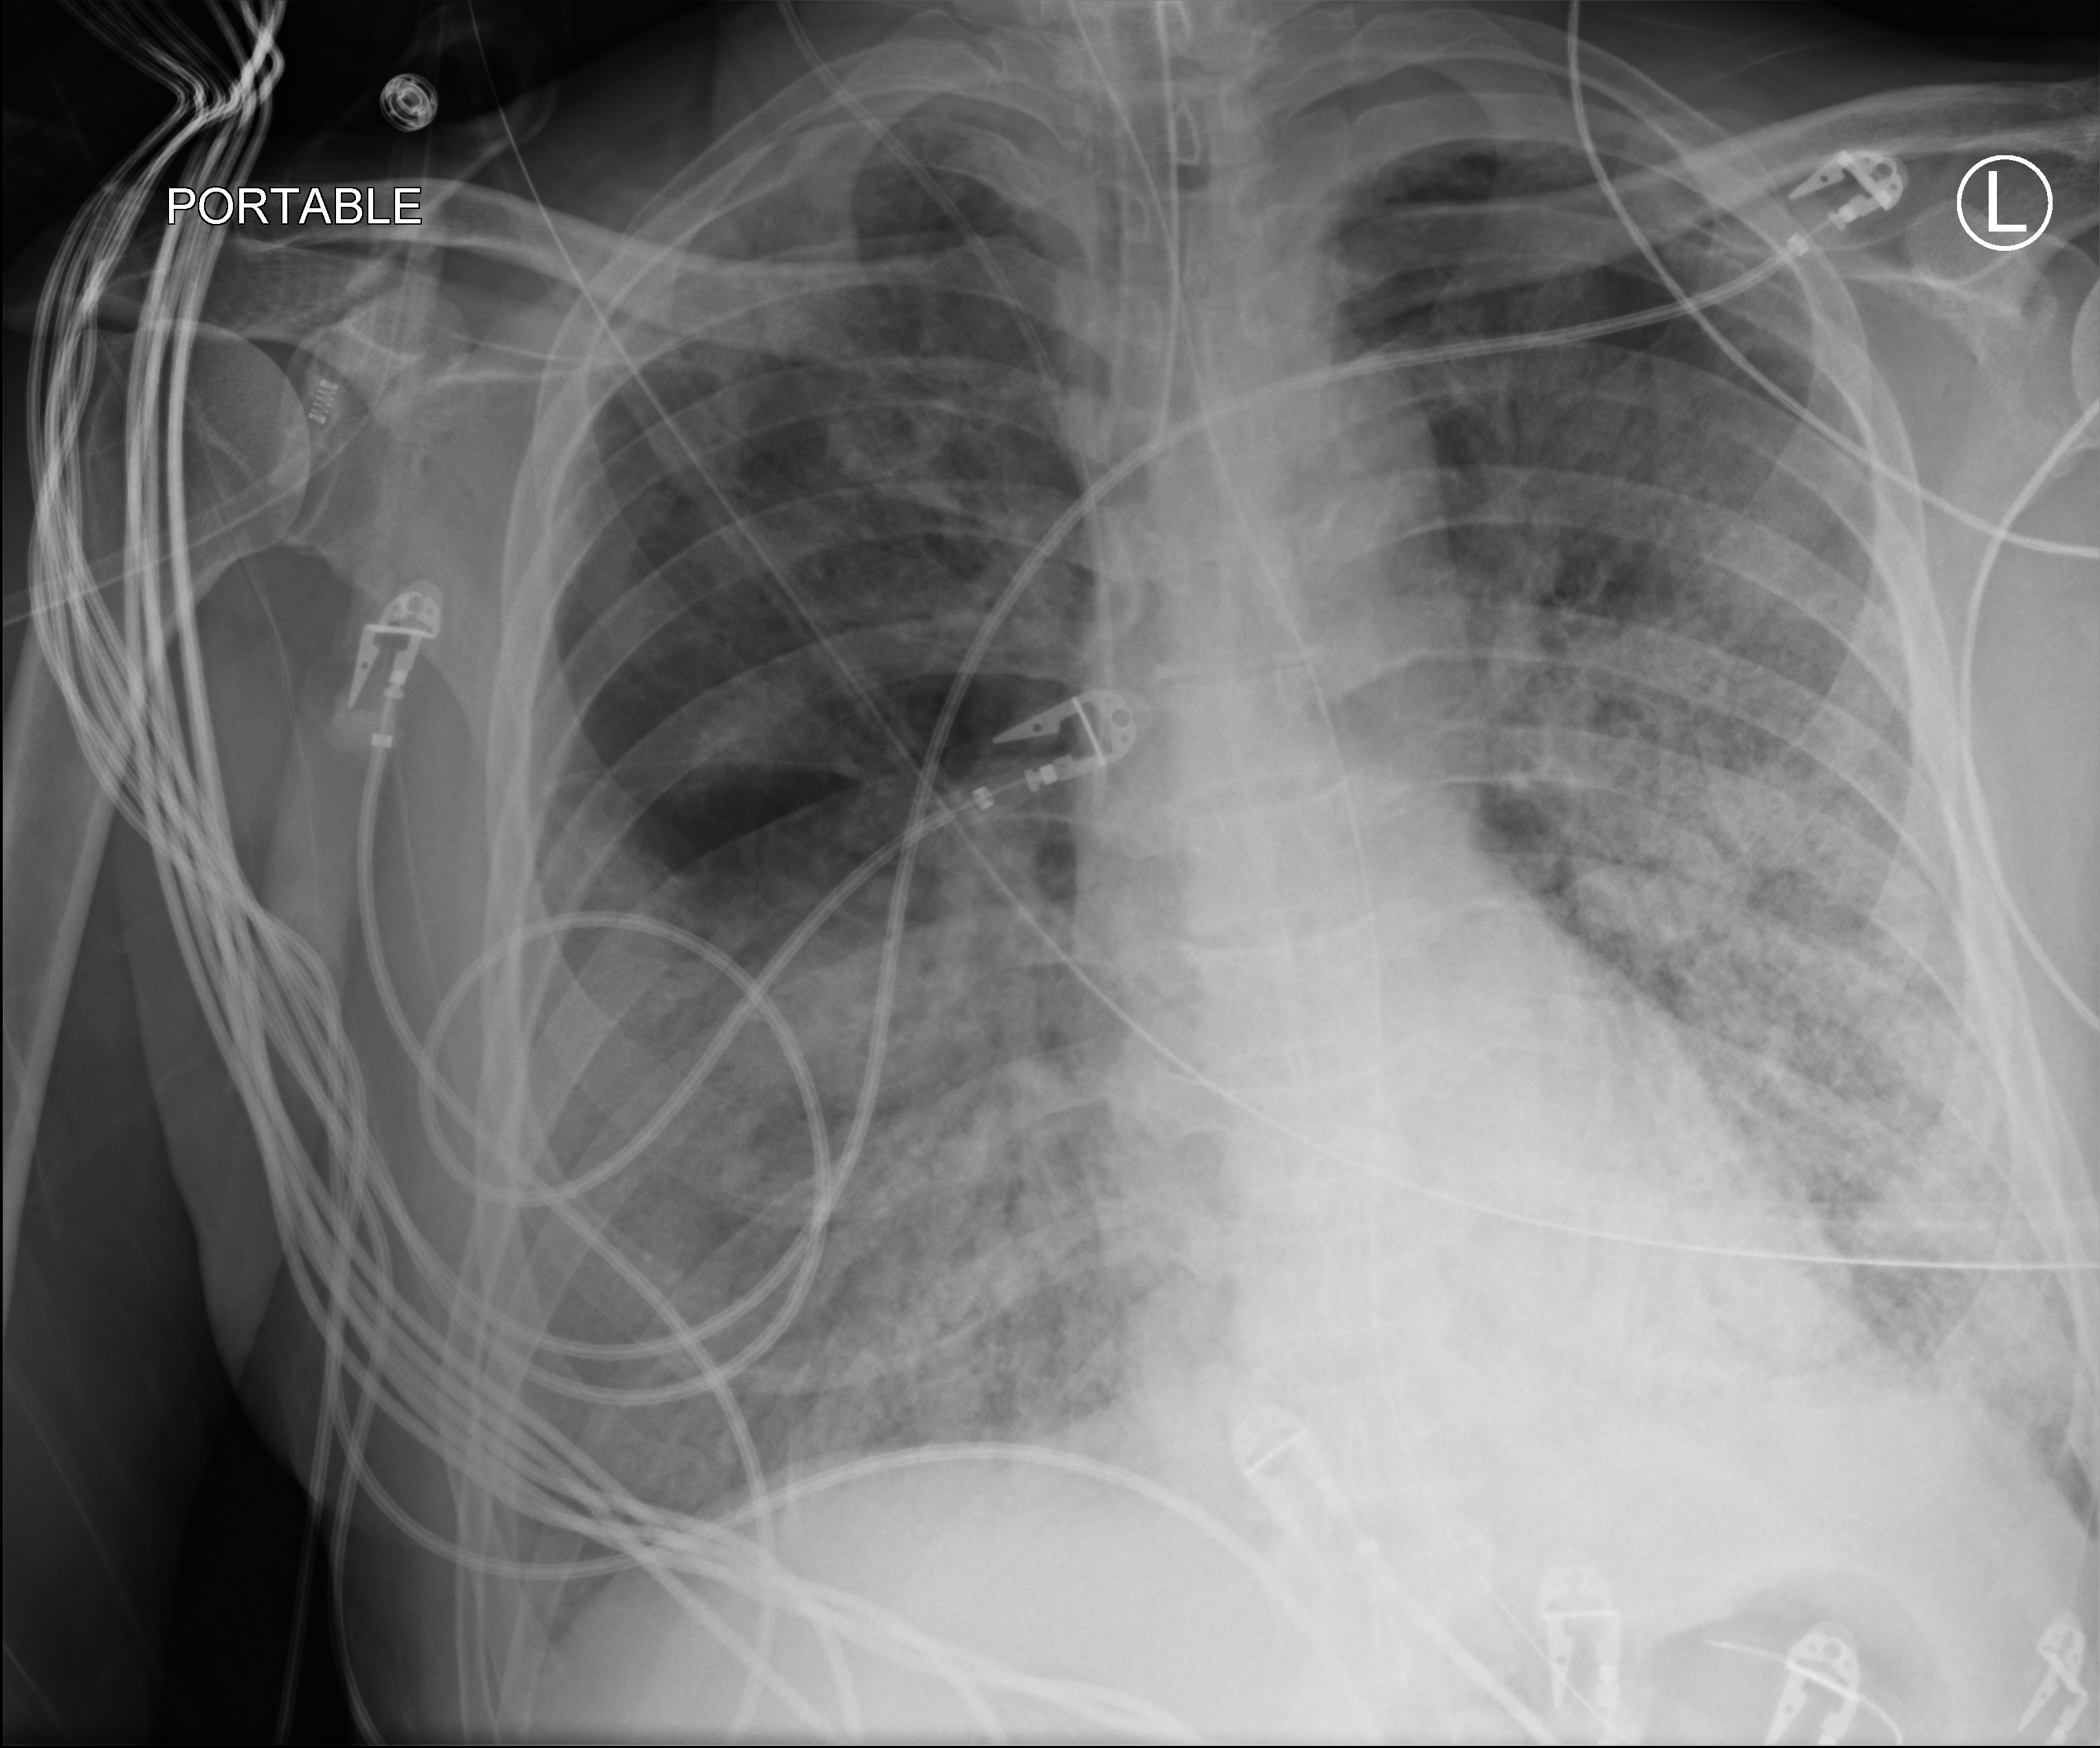
Bedside chest radiograph (computed radiography). Patient hospitalised with COVID-19; male, aged 60–74 years.
From the hospital-stay record, not from the radiograph (when in the stay this image was taken is not recorded):
- length of hospital stay: 31 days
- mechanically ventilated during this hospital stay: yes